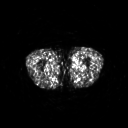
FDG PET of an extremity soft-tissue mass (from a PET/CT study), one axial slice; position 228 of 311 along the scan axis; 3.27 mm slice thickness; 128 × 128 image matrix. Male patient, age 29 years. Case-level facts recorded for this patient, not image findings: histological type: mixoid liposarcoma; grade: low; site of the primary tumour: left thigh.
Outlined on this slice (expert contour drawn on MRI and transferred to this co-registered scan by the dataset authors):
- gross tumour volume (mass): box from (x=74, y=59) to (x=80, y=64) px